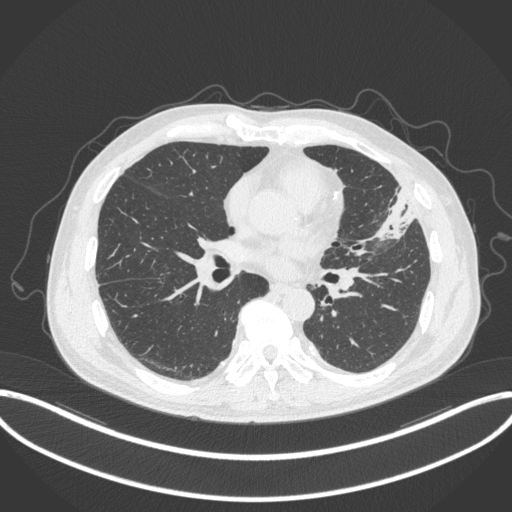
Chest CT, one axial slice; slice 160 of 382 in the series (ordered by position); reconstruction kernel B31f; 120 kVp; lung window (W 1500 / L -600 HU); 1 mm slice thickness; 512 × 512 image matrix, field of view 415 × 415 mm. Patient: male, 64 years. Case-level facts recorded for this patient, not image findings: clinical TNM (as recorded): T4 N1 M0; histopathological grade: G3.
Outlined on this slice (bounding box drawn by a radiologist):
- lung tumour (recorded histology: adenocarcinoma): bounding box <362,188,415,249> (left, top, right, bottom; pixels)